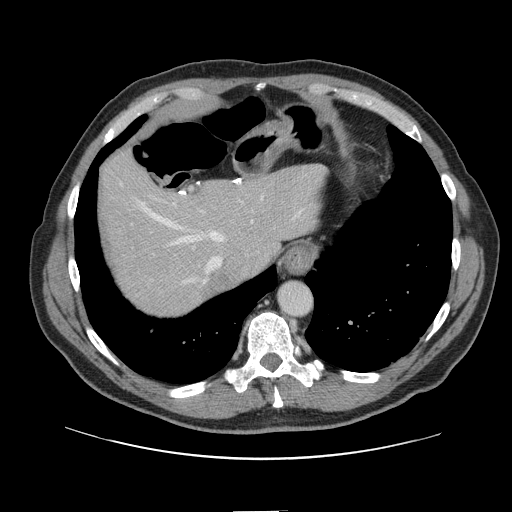
Contrast-enhanced abdominal CT, one axial slice; slice 119 of 161 in the series (ordered by position); 120 kVp; soft-tissue window (W 400 / L 40 HU); 2.5 mm slice thickness; 512 × 512 image matrix, field of view 412 × 412 mm. Male patient, age 66 years. From the clinical record (not read from this slice): diagnosis: colorectal cancer liver metastases, imaged before liver resection; multiple liver metastases: no.
Annotated regions visible in this slice (expert manual segmentation):
- hepatic veins: box from (x=121, y=184) to (x=302, y=284) px
- liver: (x=99, y=155)–(x=322, y=315)
- planned liver remnant (the part of the liver to remain after resection): (x=99, y=154)–(x=322, y=300)
- portal vein (with intrahepatic branches): (x=173, y=203)–(x=175, y=205)
- liver metastasis: (x=202, y=262)–(x=228, y=299)